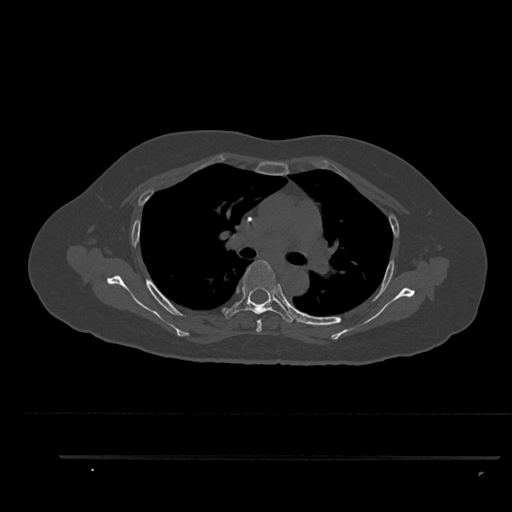
CT including the spine, one axial slice; position 611 of 797 along the scan axis; reconstruction kernel Br40s/3; bone window (W 1800 / L 400 HU); 0.5 mm slice thickness; 512 × 512 image matrix. Patient: female, 44 years. From the clinical record (not read from this slice): primary cancer: renal; vertebrae with lytic lesions (as recorded): L1.
Annotated regions visible in this slice (semi-automatically segmented with operator editing):
- T4 vertebra: bounding box (x1, y1, x2, y2) in pixels: (256, 319, 262, 333)
- T5 vertebra: (222, 260, 295, 323)